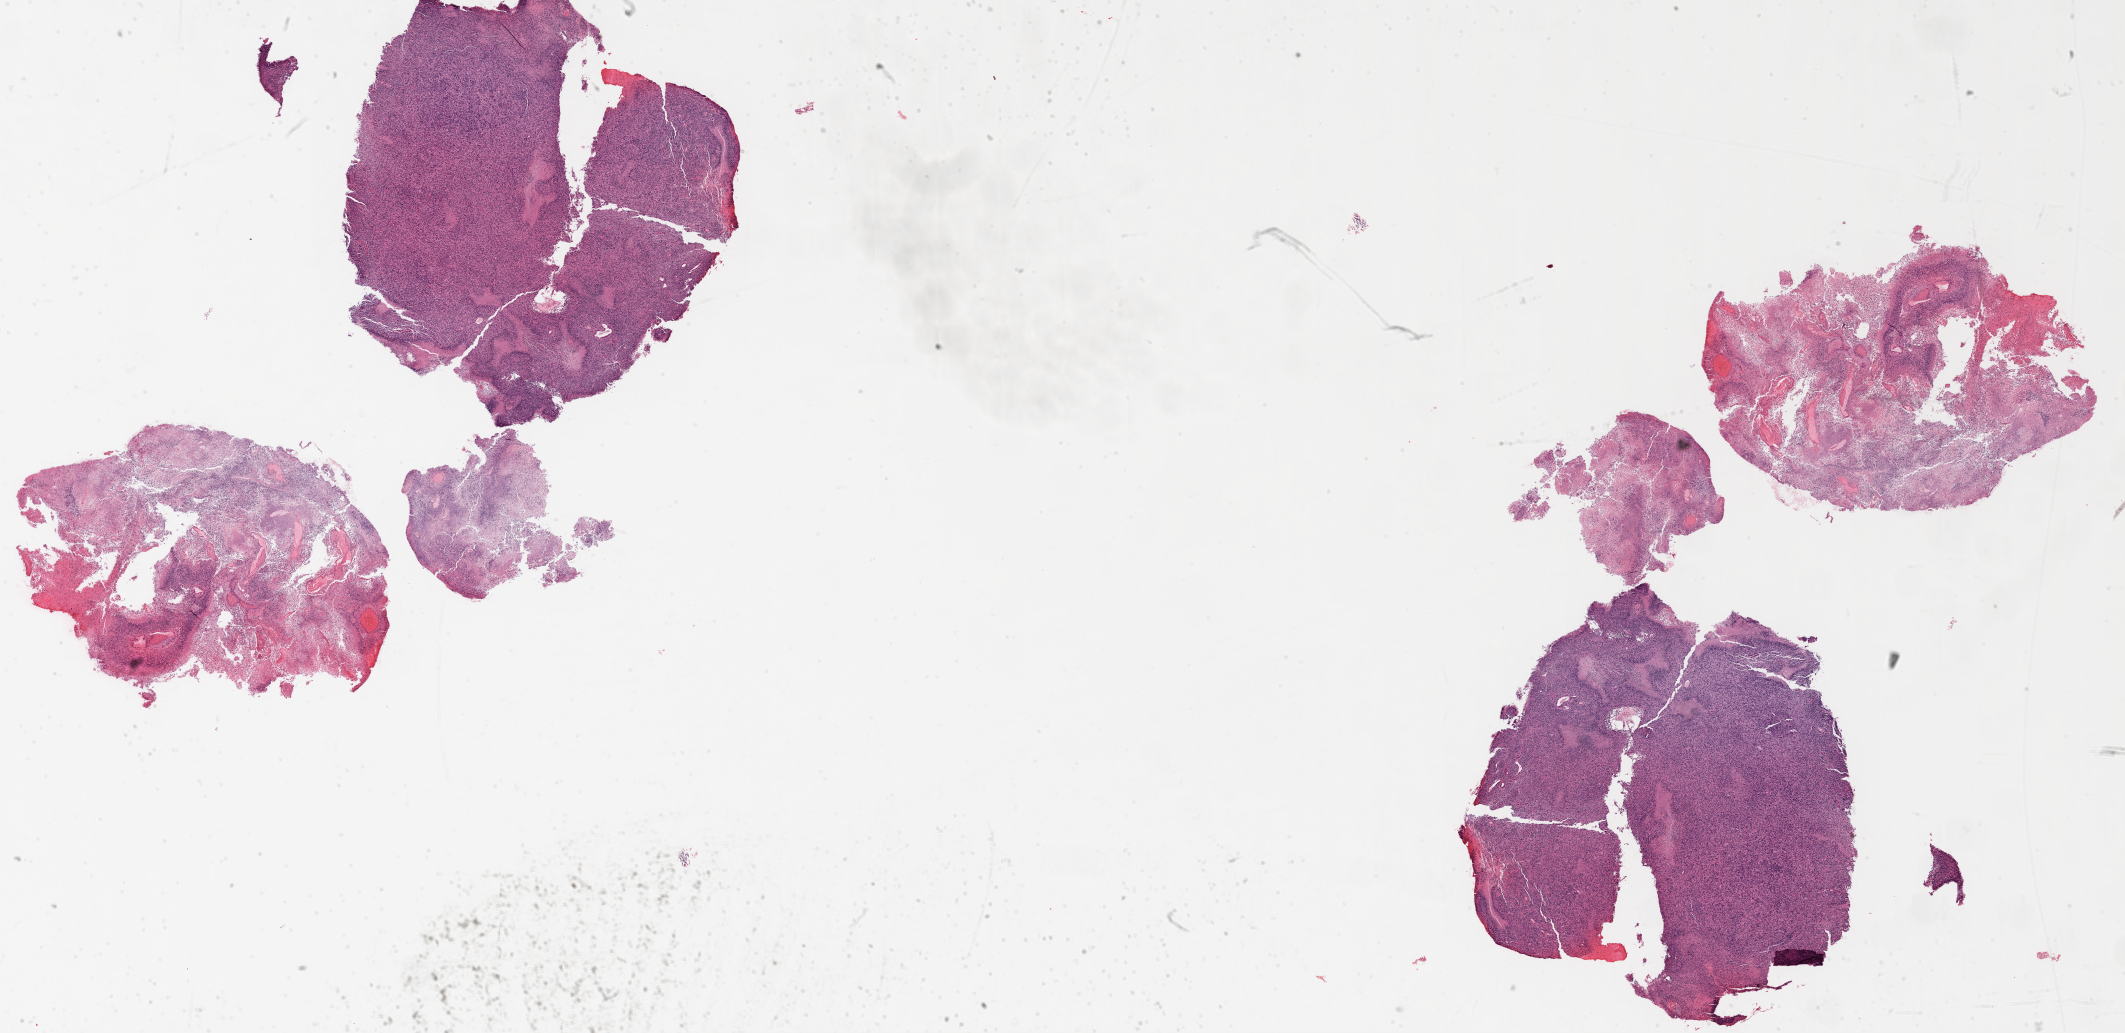
Whole-slide histology image, H&E — a low-resolution overview of the entire scanned area, about 34.1 x 16.6 mm. Formalin-fixed paraffin-embedded (FFPE) diagnostic section. Primary tumour sample from the brain. Male patient; age at initial diagnosis 66 years.
Histologic diagnosis: Glioblastoma.